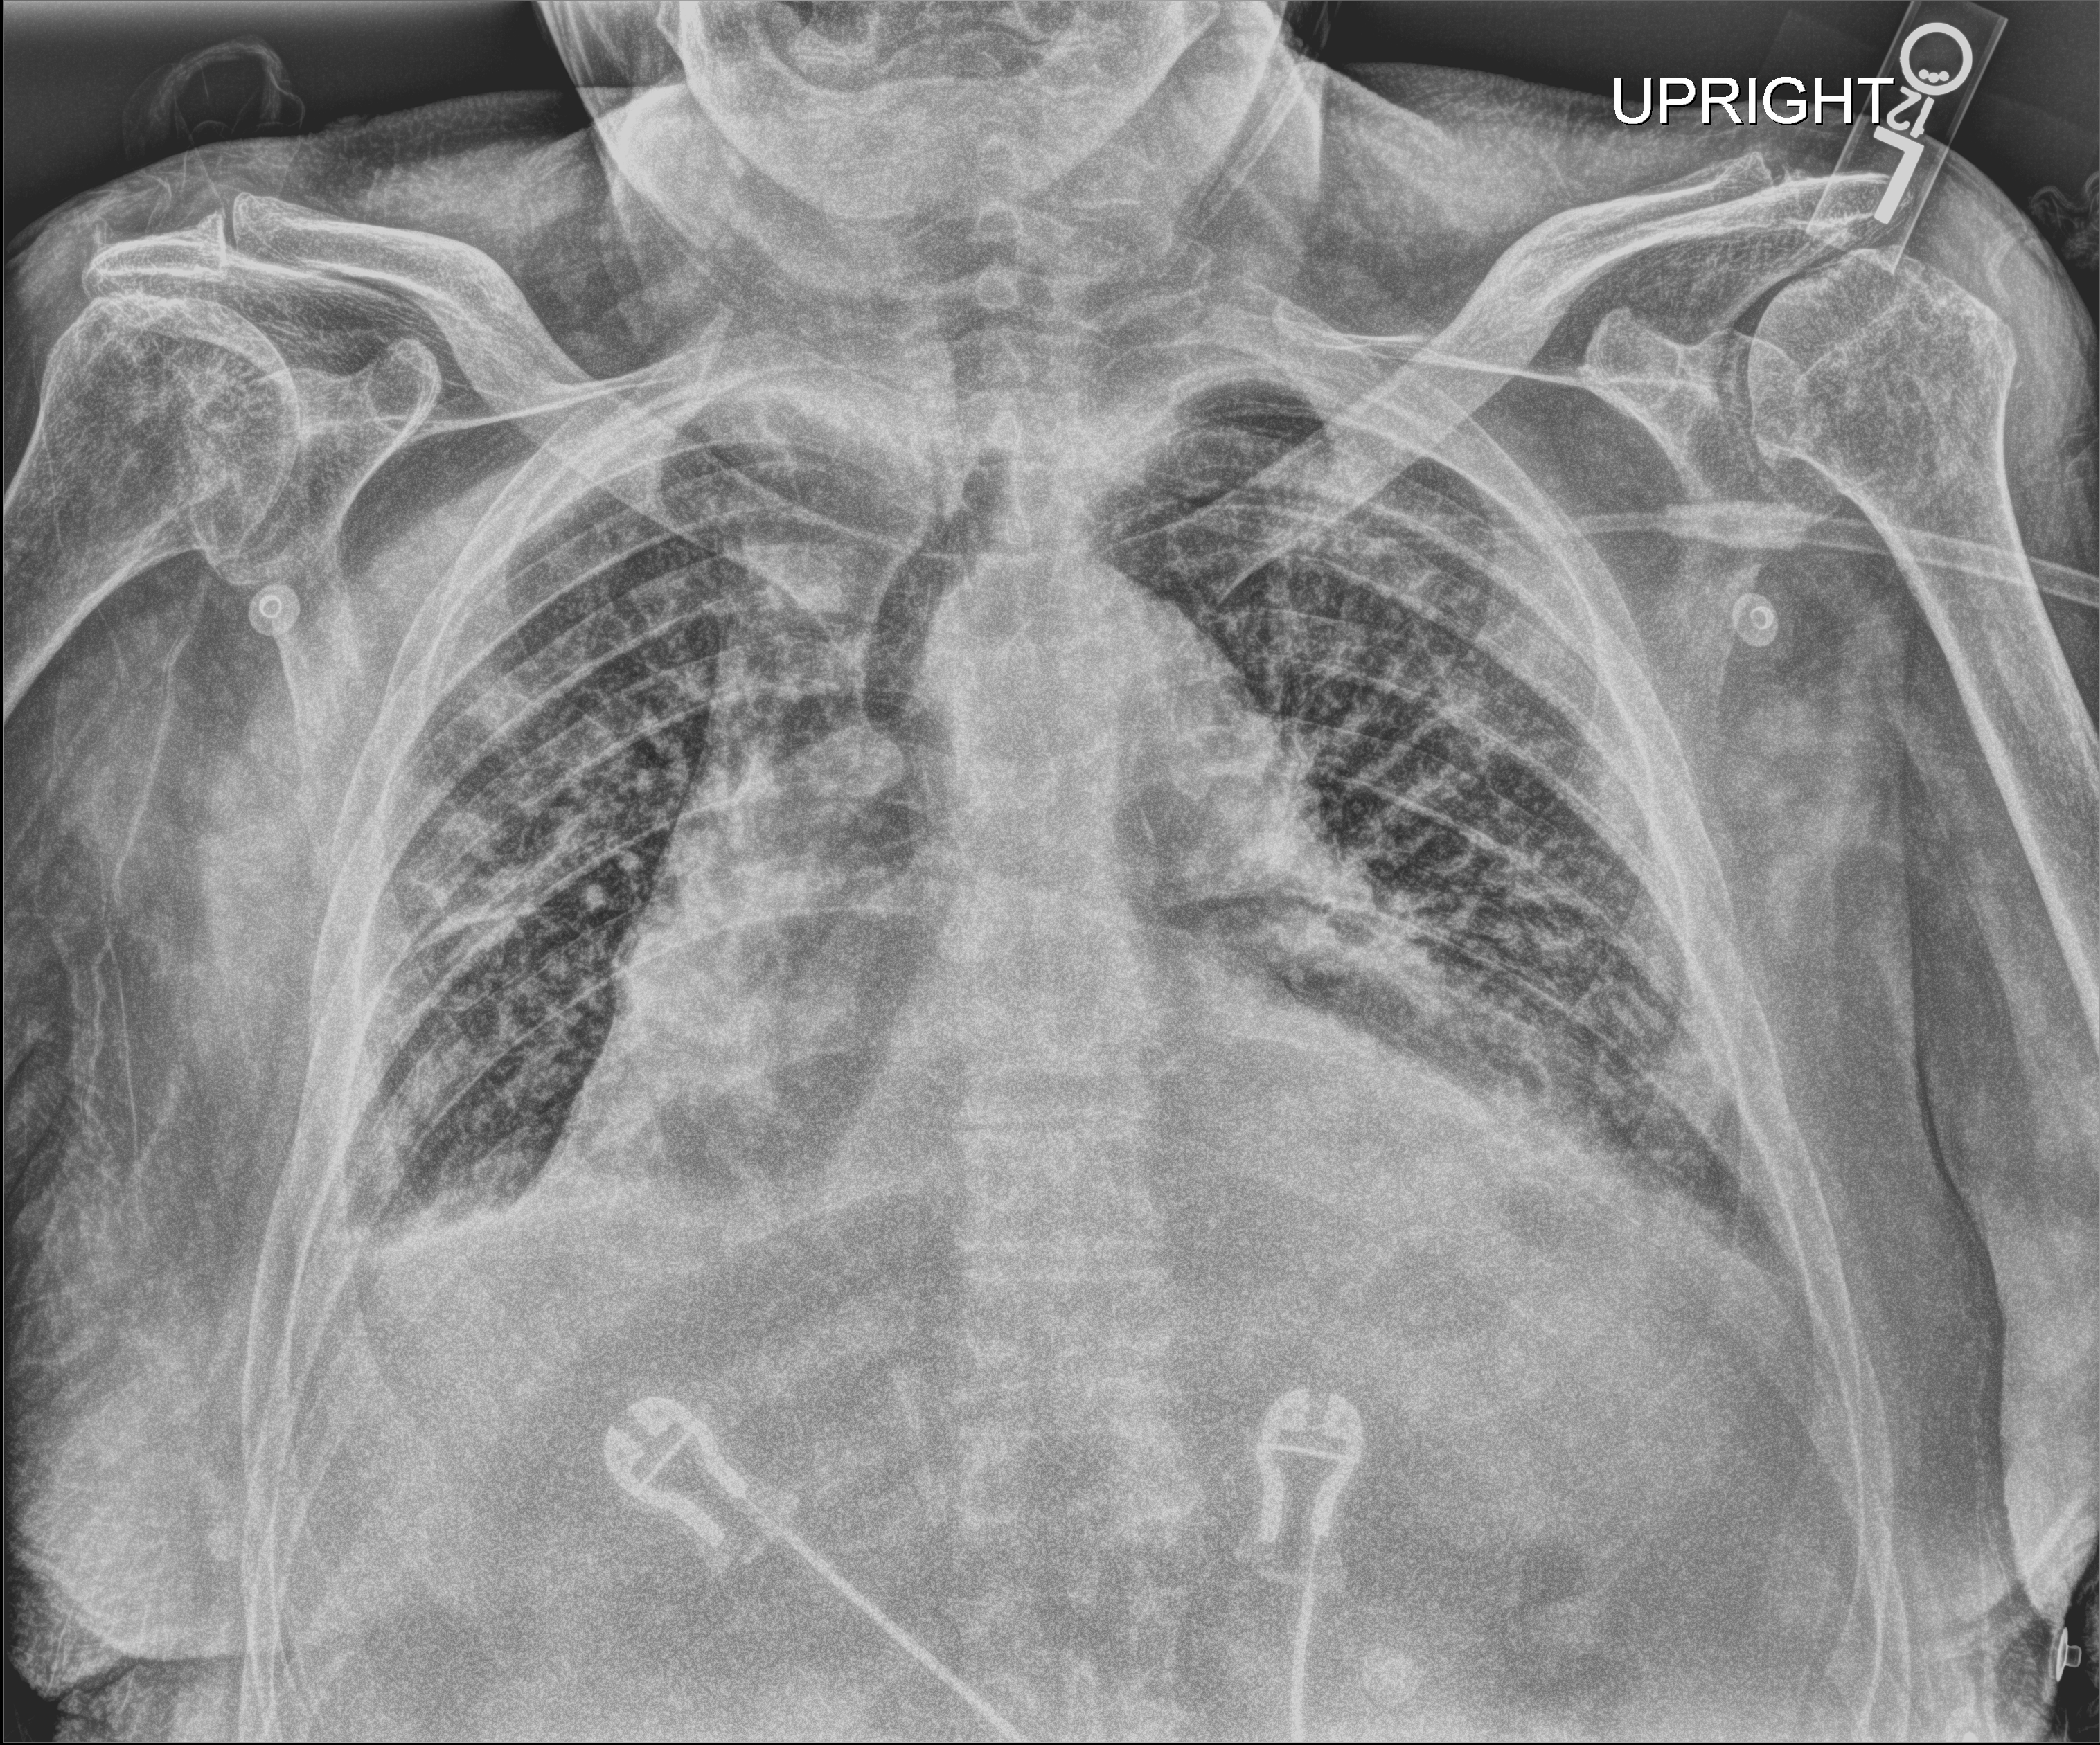
Chest radiograph (digital radiography), anteroposterior (AP) projection. Male patient hospitalised with COVID-19, age 75–90 years.
Admission-level facts for this patient (not findings on this image; timing relative to this image not recorded):
- length of hospital stay: 20 days
- mechanically ventilated during this hospital stay: no
- admitted to intensive care during this hospital stay: no